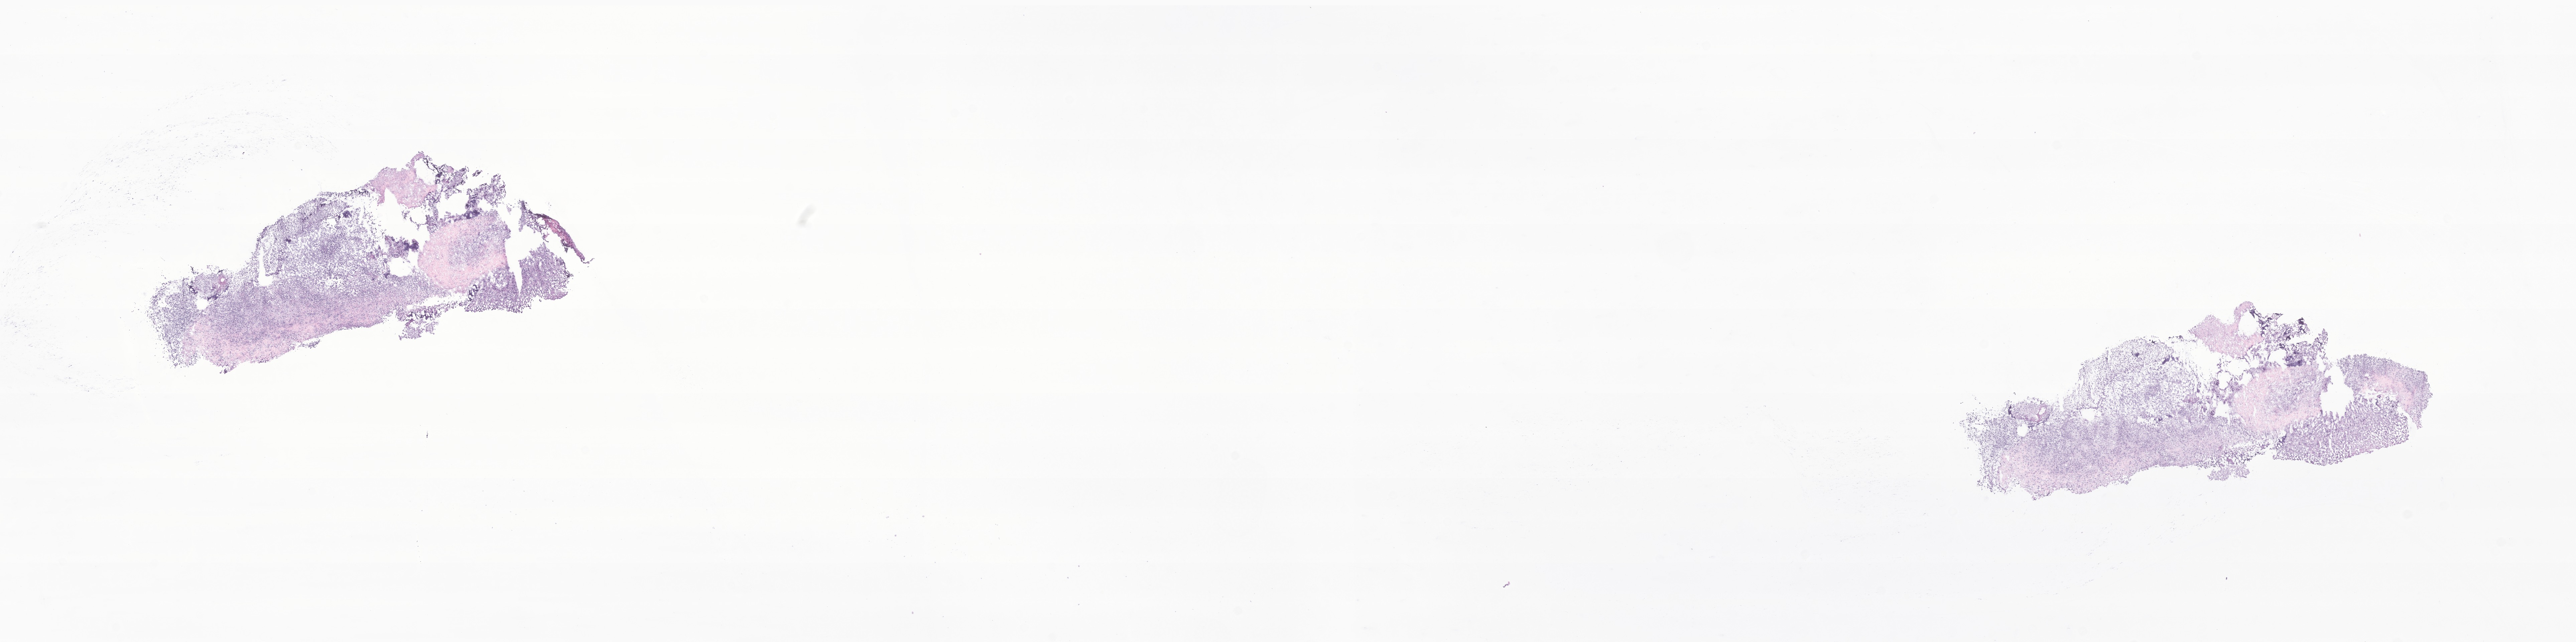
Hematoxylin and eosin (H&E) whole-slide image of tumor tissue from the brain — low-resolution overview of the scanned area, about 32.5 x 8.1 mm, frozen section. Female patient, age 177 months (14 years 9 months).
• recorded diagnosis: Neoplasm, malignant